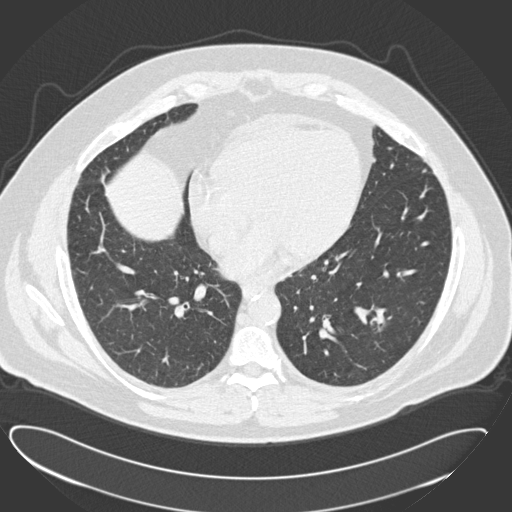
Low-dose screening chest CT, axial slice. First (baseline) screen. Lung window (W 1500 / L -600 HU). Standard (soft-tissue) reconstruction kernel (B30f). Slice 88 of 183 in the series. Male, age 57 years at enrolment. Current smoker at enrolment.
Lesion marked by an expert reader, box from (x=352, y=296) to (x=407, y=347) px. The screening reader recorded 2 non-calcified nodules or masses ≥4 mm on this exam; which of them this box marks is not recorded. Official screen result: positive, change unspecified: nodule(s) >= 4 mm or enlarging nodule(s), mass(es), or other non-specific abnormalities suspicious for lung cancer. Participant outcome: lung cancer diagnosed 791 days after this screen (after the third annual screen) — squamous cell carcinoma, NOS, left lower lobe, moderately differentiated (G2), stage IA (AJCC 6th edition), 22 mm at pathology.